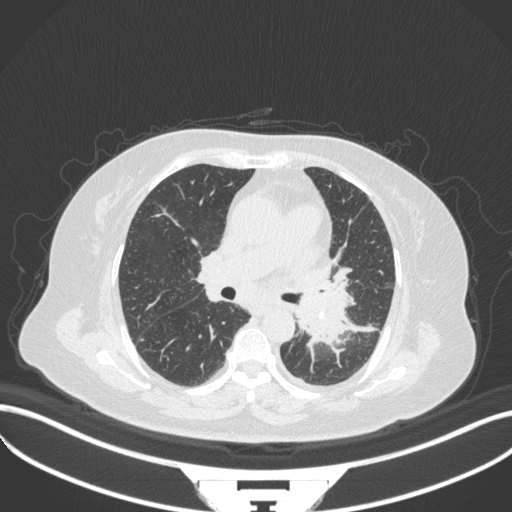
Chest CT, one axial slice; slice 197 of 328 in the series (ordered by position); reconstruction kernel B31f; 120 kVp; lung window (W 1500 / L -600 HU); 1 mm slice thickness; 512 × 512 image matrix, field of view 400 × 400 mm. Female patient, age 69 years. From the clinical record (not read from this slice): clinical TNM (as recorded): T2b N3 M1.
Outlined on this slice (rectangle marked by the reading radiologist):
- lung tumour (recorded histology: adenocarcinoma): box from (x=294, y=278) to (x=354, y=353) px